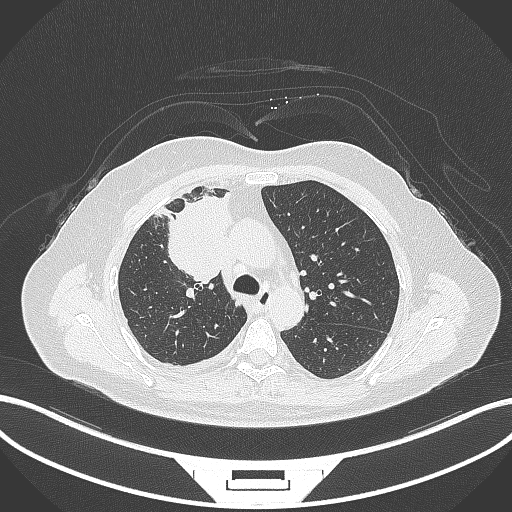
Chest CT, one axial slice. Position 196 of 305 along the scan axis. Reconstruction kernel B70f. 120 kVp. Lung window (W 1500 / L -600 HU). 512 × 512 image matrix. Patient: female, 52 years. Case-level facts recorded for this patient, not image findings: clinical TNM (as recorded): T3 N1 M1.
Outlined on this slice (bounding box drawn by a radiologist):
- lung tumour (recorded histology: adenocarcinoma): bounding box (x1, y1, x2, y2) in pixels: (148, 186, 234, 289)